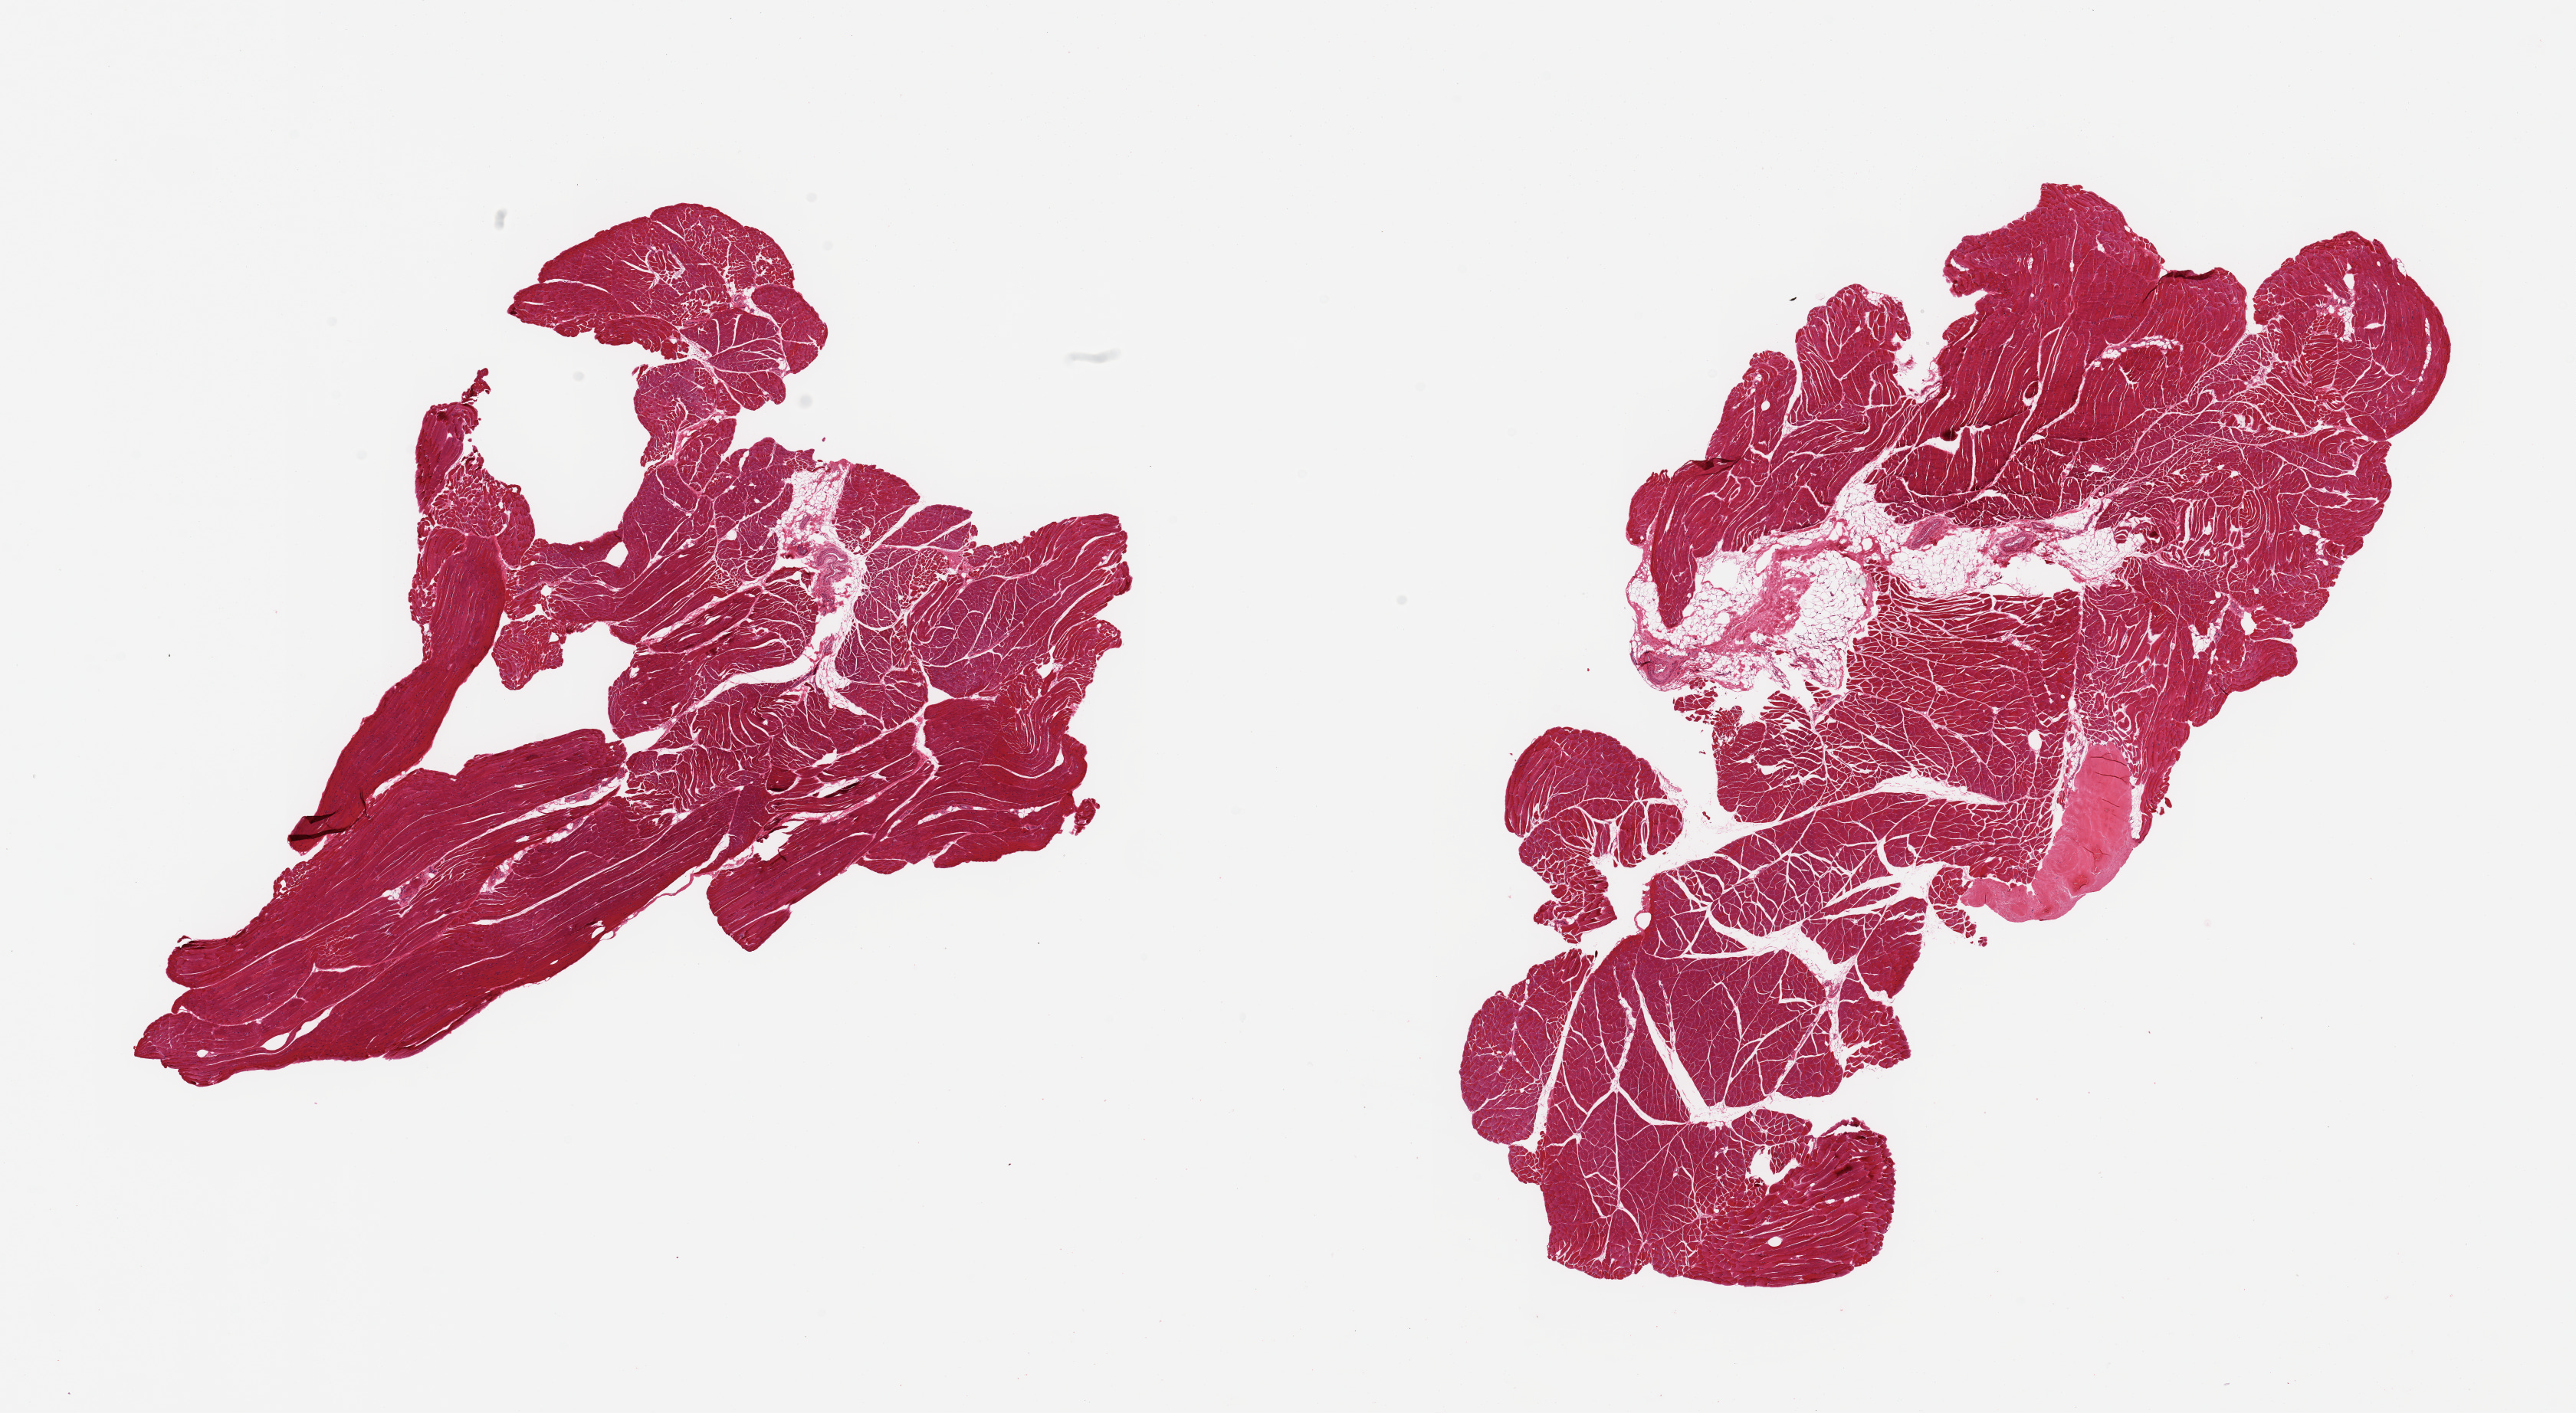
Whole-slide image, hematoxylin and eosin (H&E) stain — a low-resolution overview of the entire scanned area, about 26.6 x 14.6 mm. PAXgene-fixed, paraffin-embedded tissue. Section of skeletal muscle (target tissue). Tissue donor sample.
Review note (as recorded): 2 pieces; skeletal muscle with from 5-10% fat and tendon.